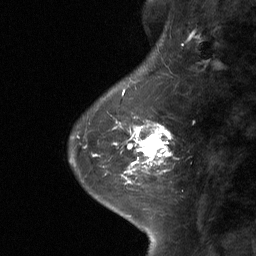
Breast MRI (dynamic contrast-enhanced), one sagittal slice. Position 19 of 64 along the scan axis. Dynamic contrast-enhanced study with each time point stored as its own series, time point 2 of 3 at this slice position (early post-contrast, ordered by acquisition time). 1.5 T. TE 4.8 ms, TR 27 ms. 256 × 256 image matrix. Patient: female, 42 years. Case-level facts recorded for this patient, not image findings: setting: breast cancer imaged before/during neoadjuvant chemotherapy; receptor status: triple-negative.
Structures marked on this image (semi-automatic segmentation, software-assisted and operator-edited):
- analysis volume of interest (the breast-tissue region the enhancement analysis was run in; not a lesion): box from (x=111, y=104) to (x=171, y=178) px
- tumour enhancement mask (voxels above the 90 % enhancement threshold inside the analysis volume of interest): (x=115, y=121)–(x=171, y=178)